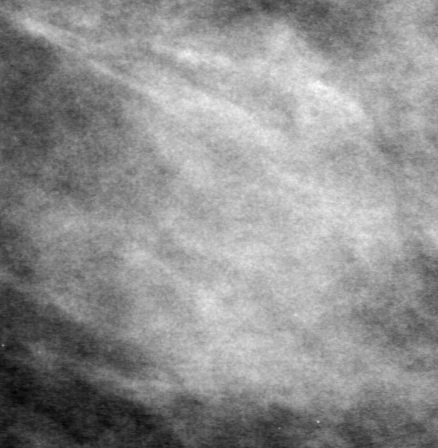
Crop from a digitized film mammogram around one marked abnormality, left breast, CC view.
Mass, shape oval, margins obscured; BI-RADS assessment category 0 (incomplete: needs additional imaging); pathology (as recorded): benign.